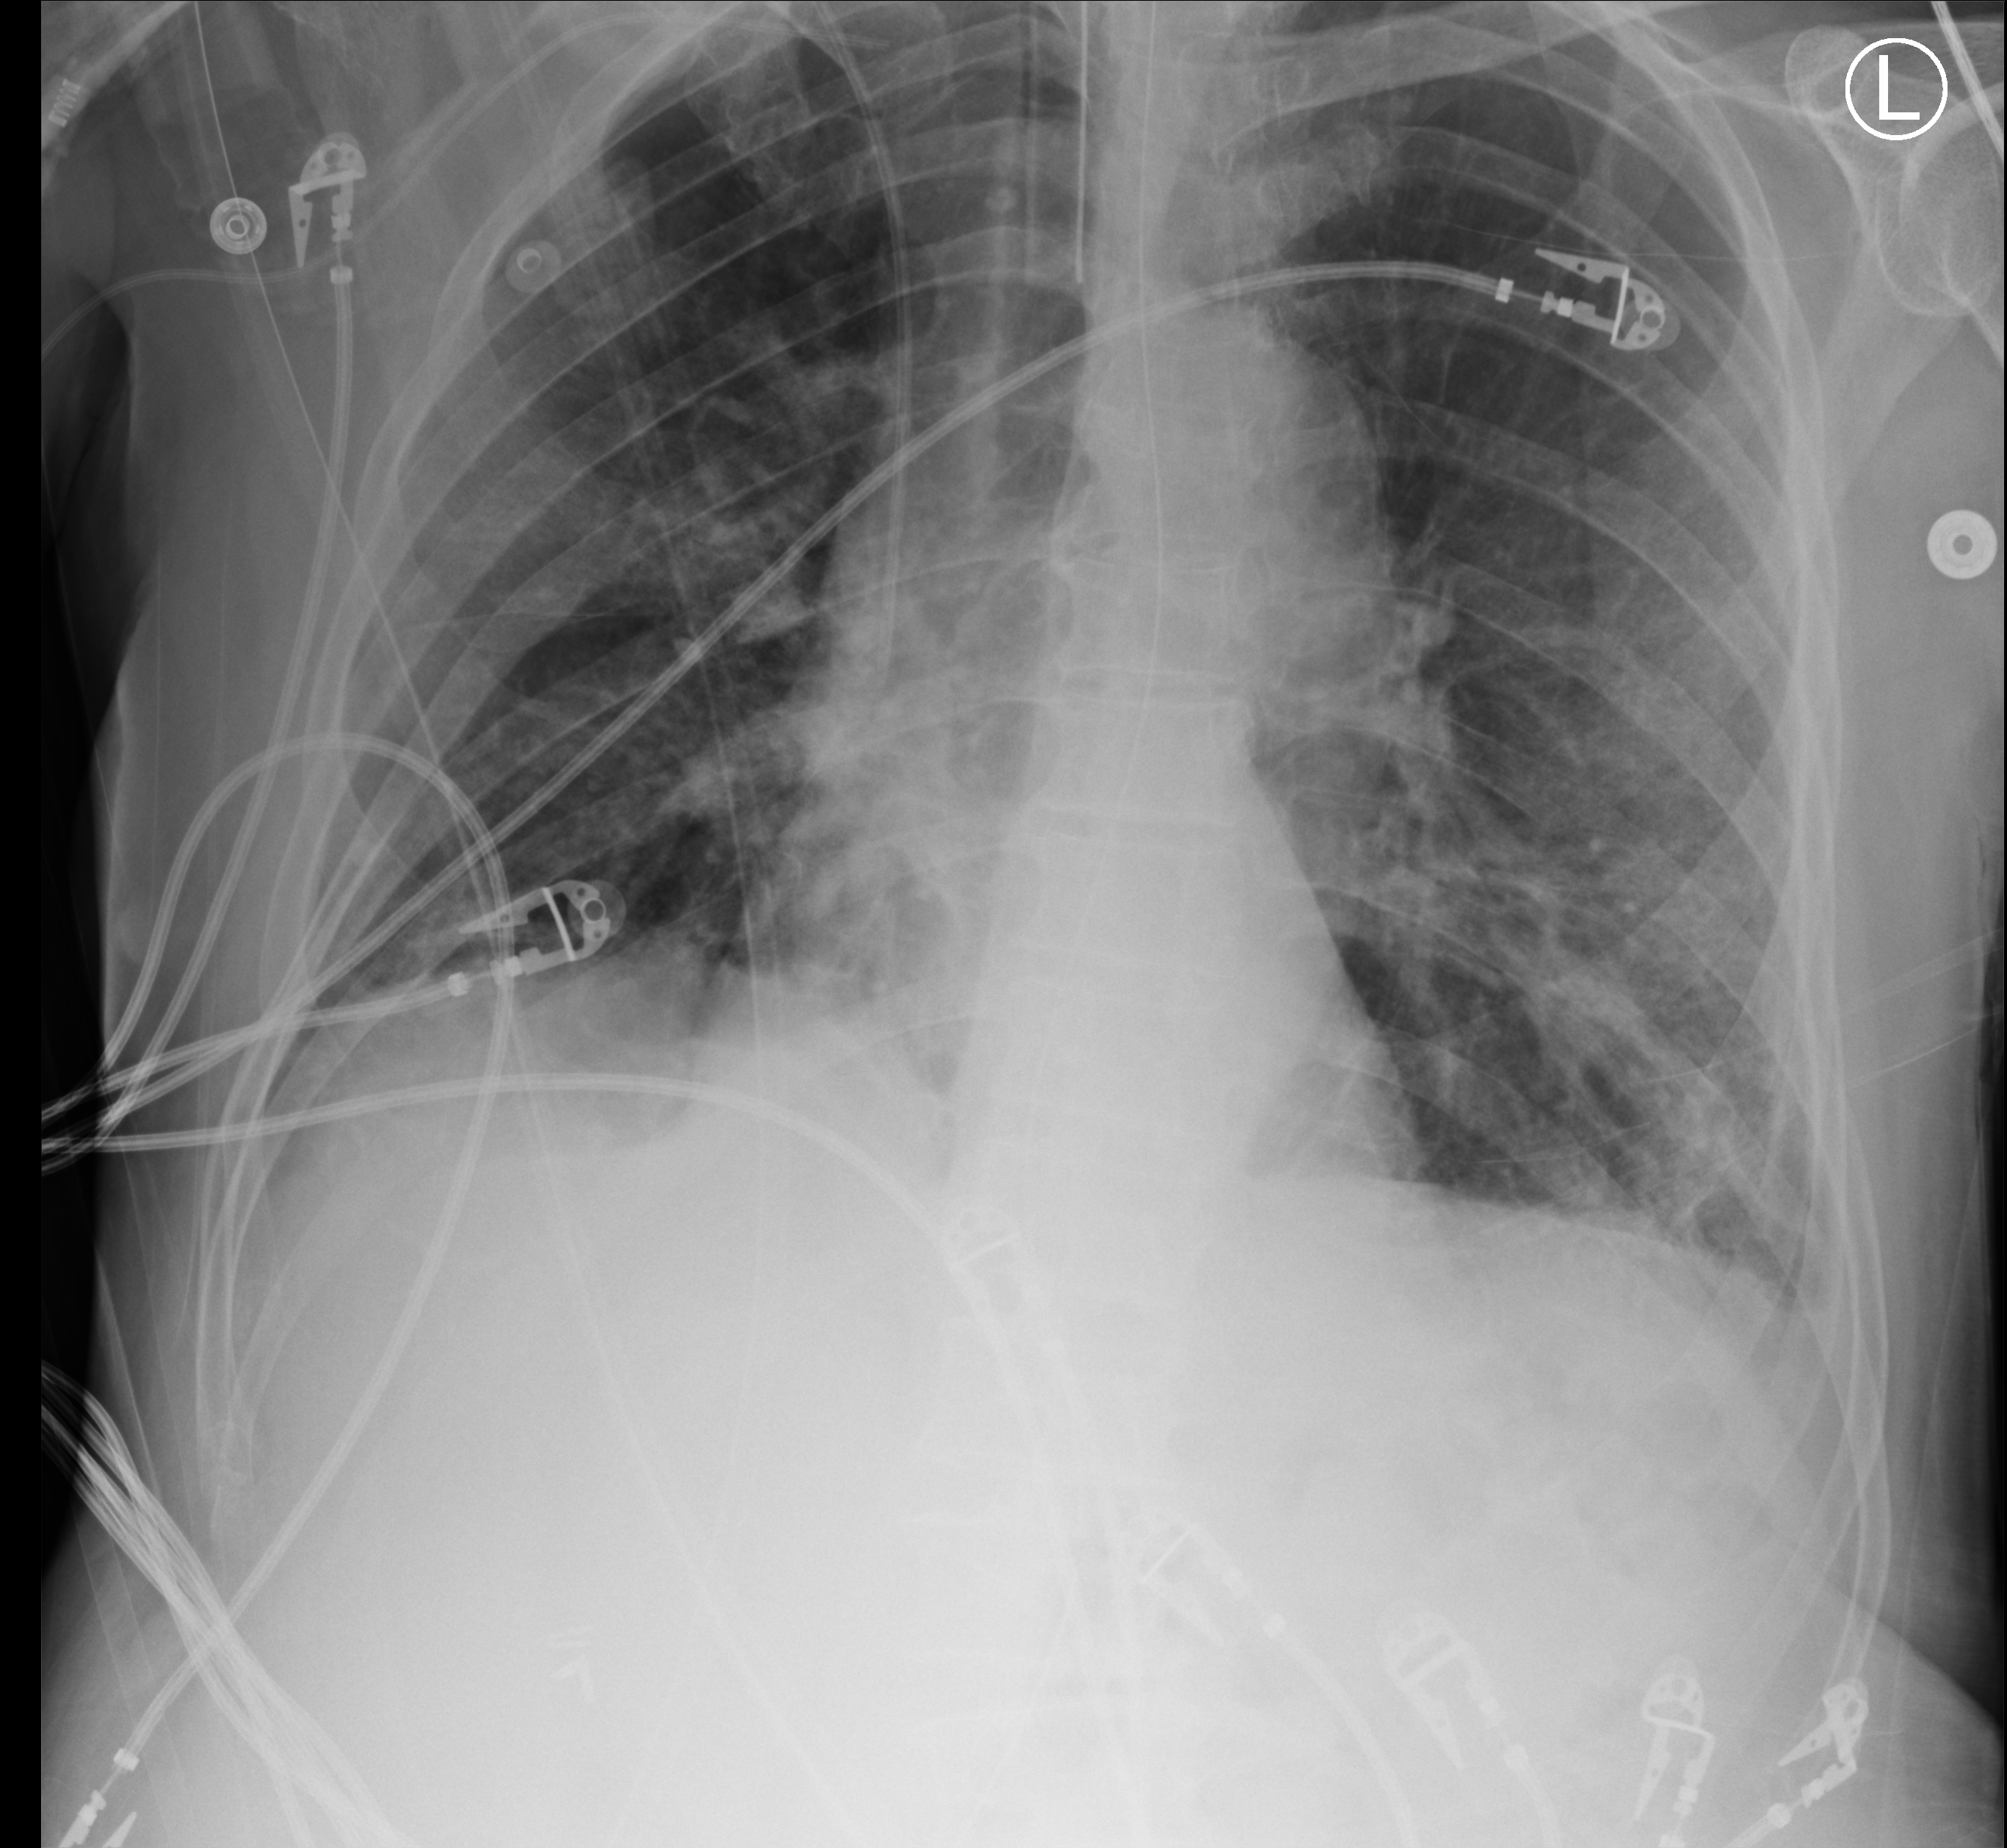
Portable chest radiograph. Patient hospitalised with COVID-19; male, aged 75–90 years.
Admission-level facts for this patient (not findings on this image; timing relative to this image not recorded): admitted to intensive care during this hospital stay: yes.